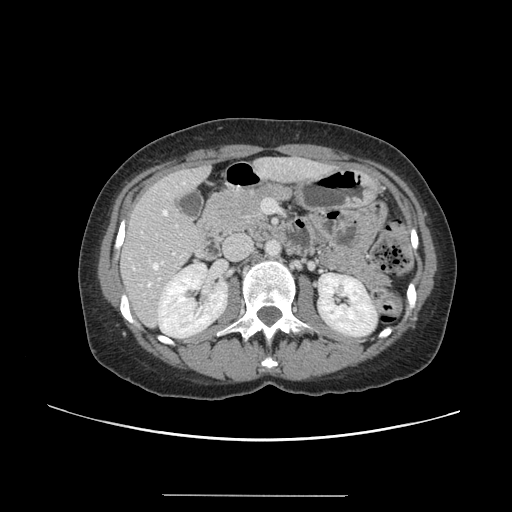
Contrast-enhanced abdominal CT, one axial slice; position 61 of 144 along the scan axis; 120 kVp; intravenous contrast given; soft-tissue window (W 400 / L 40 HU); 2.5 mm slice thickness; 512 × 512 image matrix, field of view 380 × 380 mm. Female patient, age 53 years. Case-level facts recorded for this patient, not image findings: diagnosis: colorectal cancer liver metastases, imaged before liver resection; multiple liver metastases: yes; largest metastasis: 1.1 cm; disease in both lobes: no.
Structures marked on this image (outlined manually by an expert reader):
- hepatic veins: bounding box [x1, y1, x2, y2] px = [148, 210, 167, 286]
- liver: [123, 159, 329, 326]
- planned liver remnant (the part of the liver to remain after resection): [122, 158, 326, 309]
- portal vein (with intrahepatic branches): [158, 252, 176, 281]